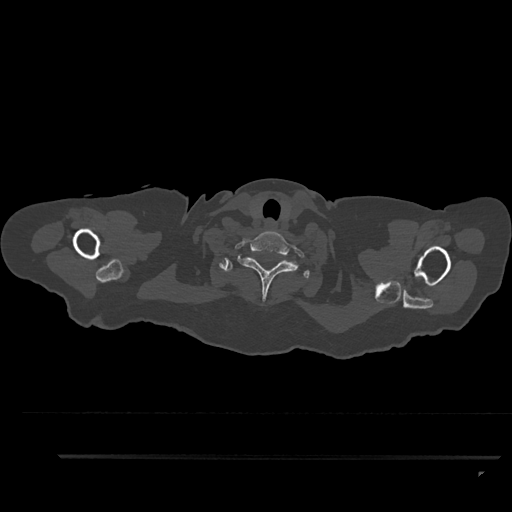
CT including the spine, one axial slice. Position 787 of 797 along the scan axis. Reconstruction kernel Br40s/3. 120 kVp. Bone window (W 1800 / L 400 HU). 0.5 mm slice thickness. 512 × 512 image matrix. Patient: female, 44 years. From the clinical record (not read from this slice): primary cancer: renal.
Outlined on this slice (semi-automatically segmented with operator editing):
- T1 vertebra: bounding box (x1, y1, x2, y2) in pixels: (220, 258, 309, 279)